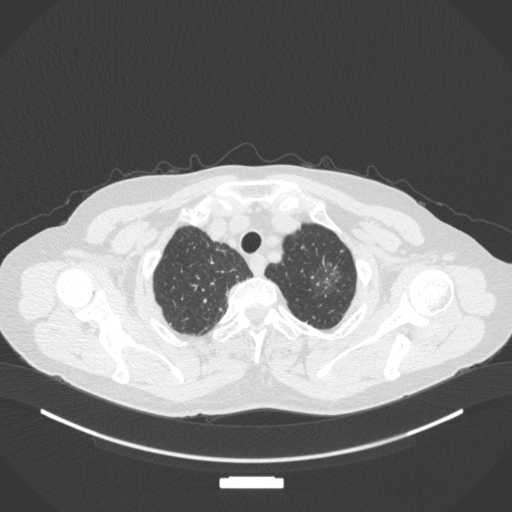
Chest CT, one axial slice; slice 318 of 369 in the series (ordered by position); 120 kVp; lung window (W 1500 / L -600 HU); 1 mm slice thickness; 512 × 512 image matrix, field of view 400 × 400 mm. Female patient, age 64 years. From the clinical record (not read from this slice): clinical TNM (as recorded): T1c N0 M0.
Outlined on this slice (rectangle marked by the reading radiologist):
- lung tumour (recorded histology: adenocarcinoma): bounding box [x1, y1, x2, y2] px = [317, 259, 342, 291]